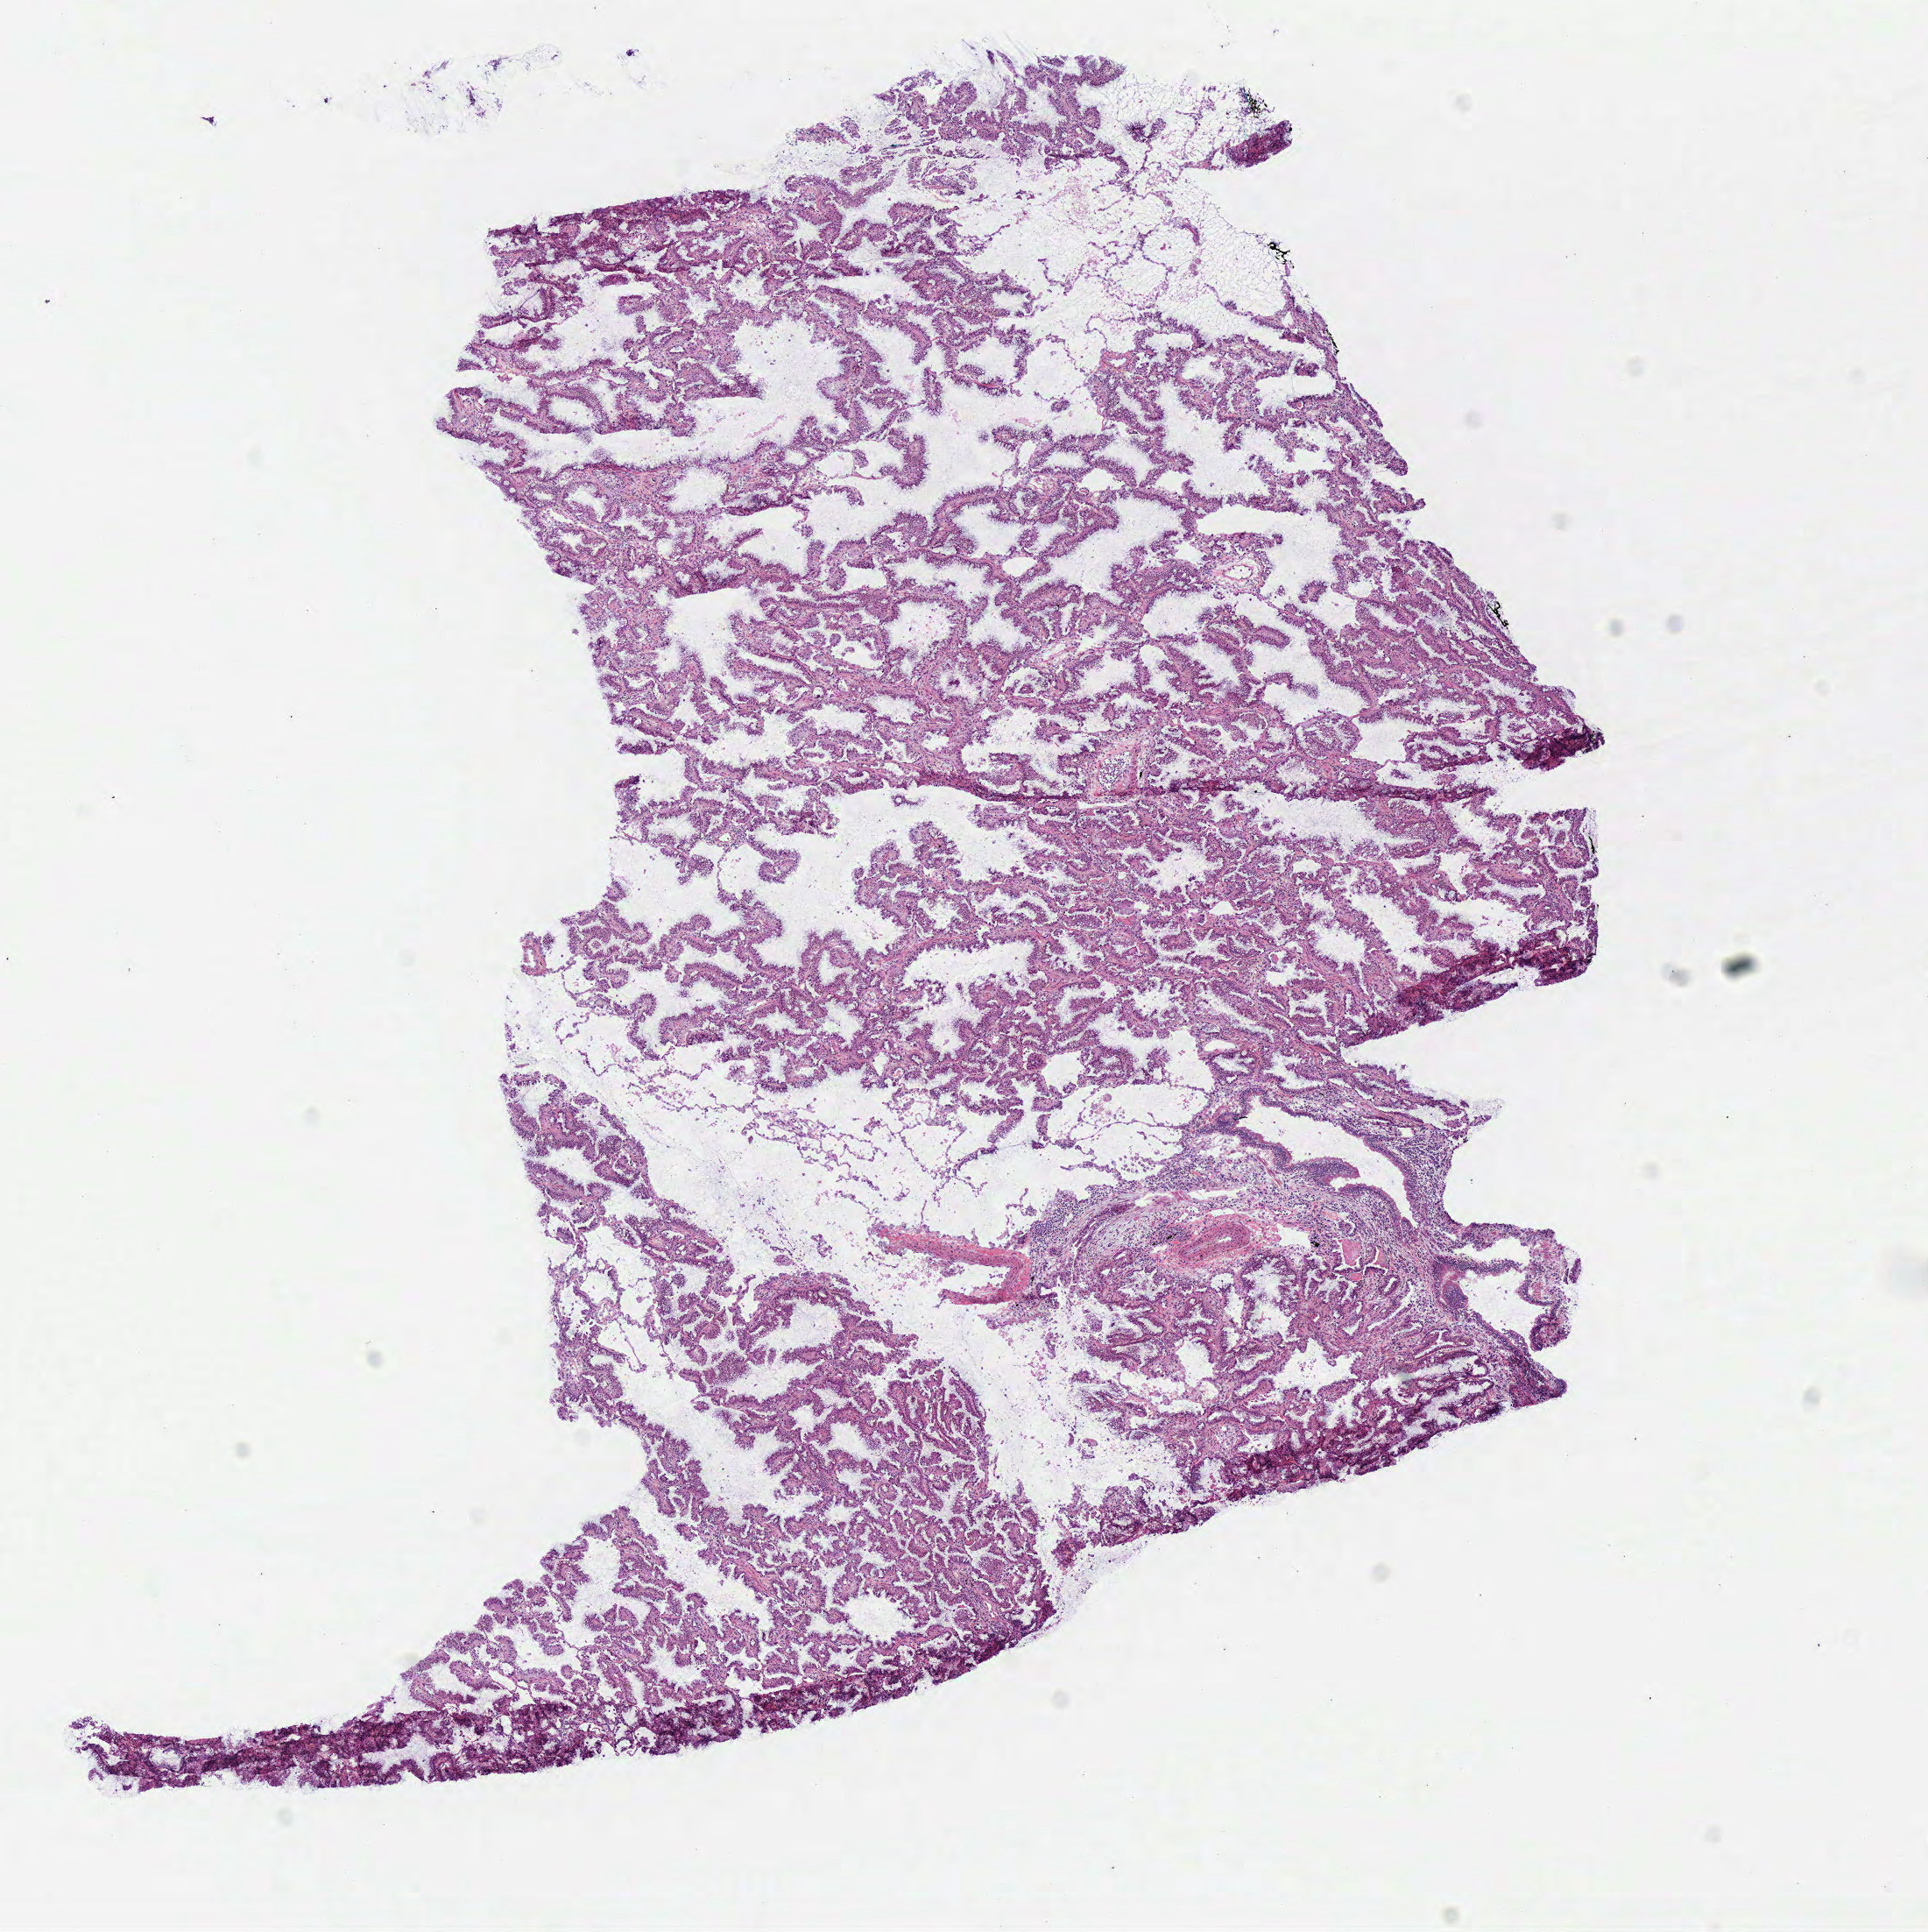
Whole-slide histology image, H&E, a low-resolution overview of the entire scanned area, about 8.7 x 8.7 mm, frozen section, primary tumour sample from the lung. Male patient; age at initial diagnosis 64 years. Slide review estimates, as recorded: tumour cells 95%, tumour nuclei 90%, normal cells 5%, stromal cells 0%, necrosis 0%. Infiltration values recorded for this section: lymphocyte infiltration 1%, monocyte infiltration 2%, neutrophil infiltration 0%.
* AJCC pathologic stage: IIB (7th edition)
* diagnosis: Mucinous adenocarcinoma (lower lobe, lung)